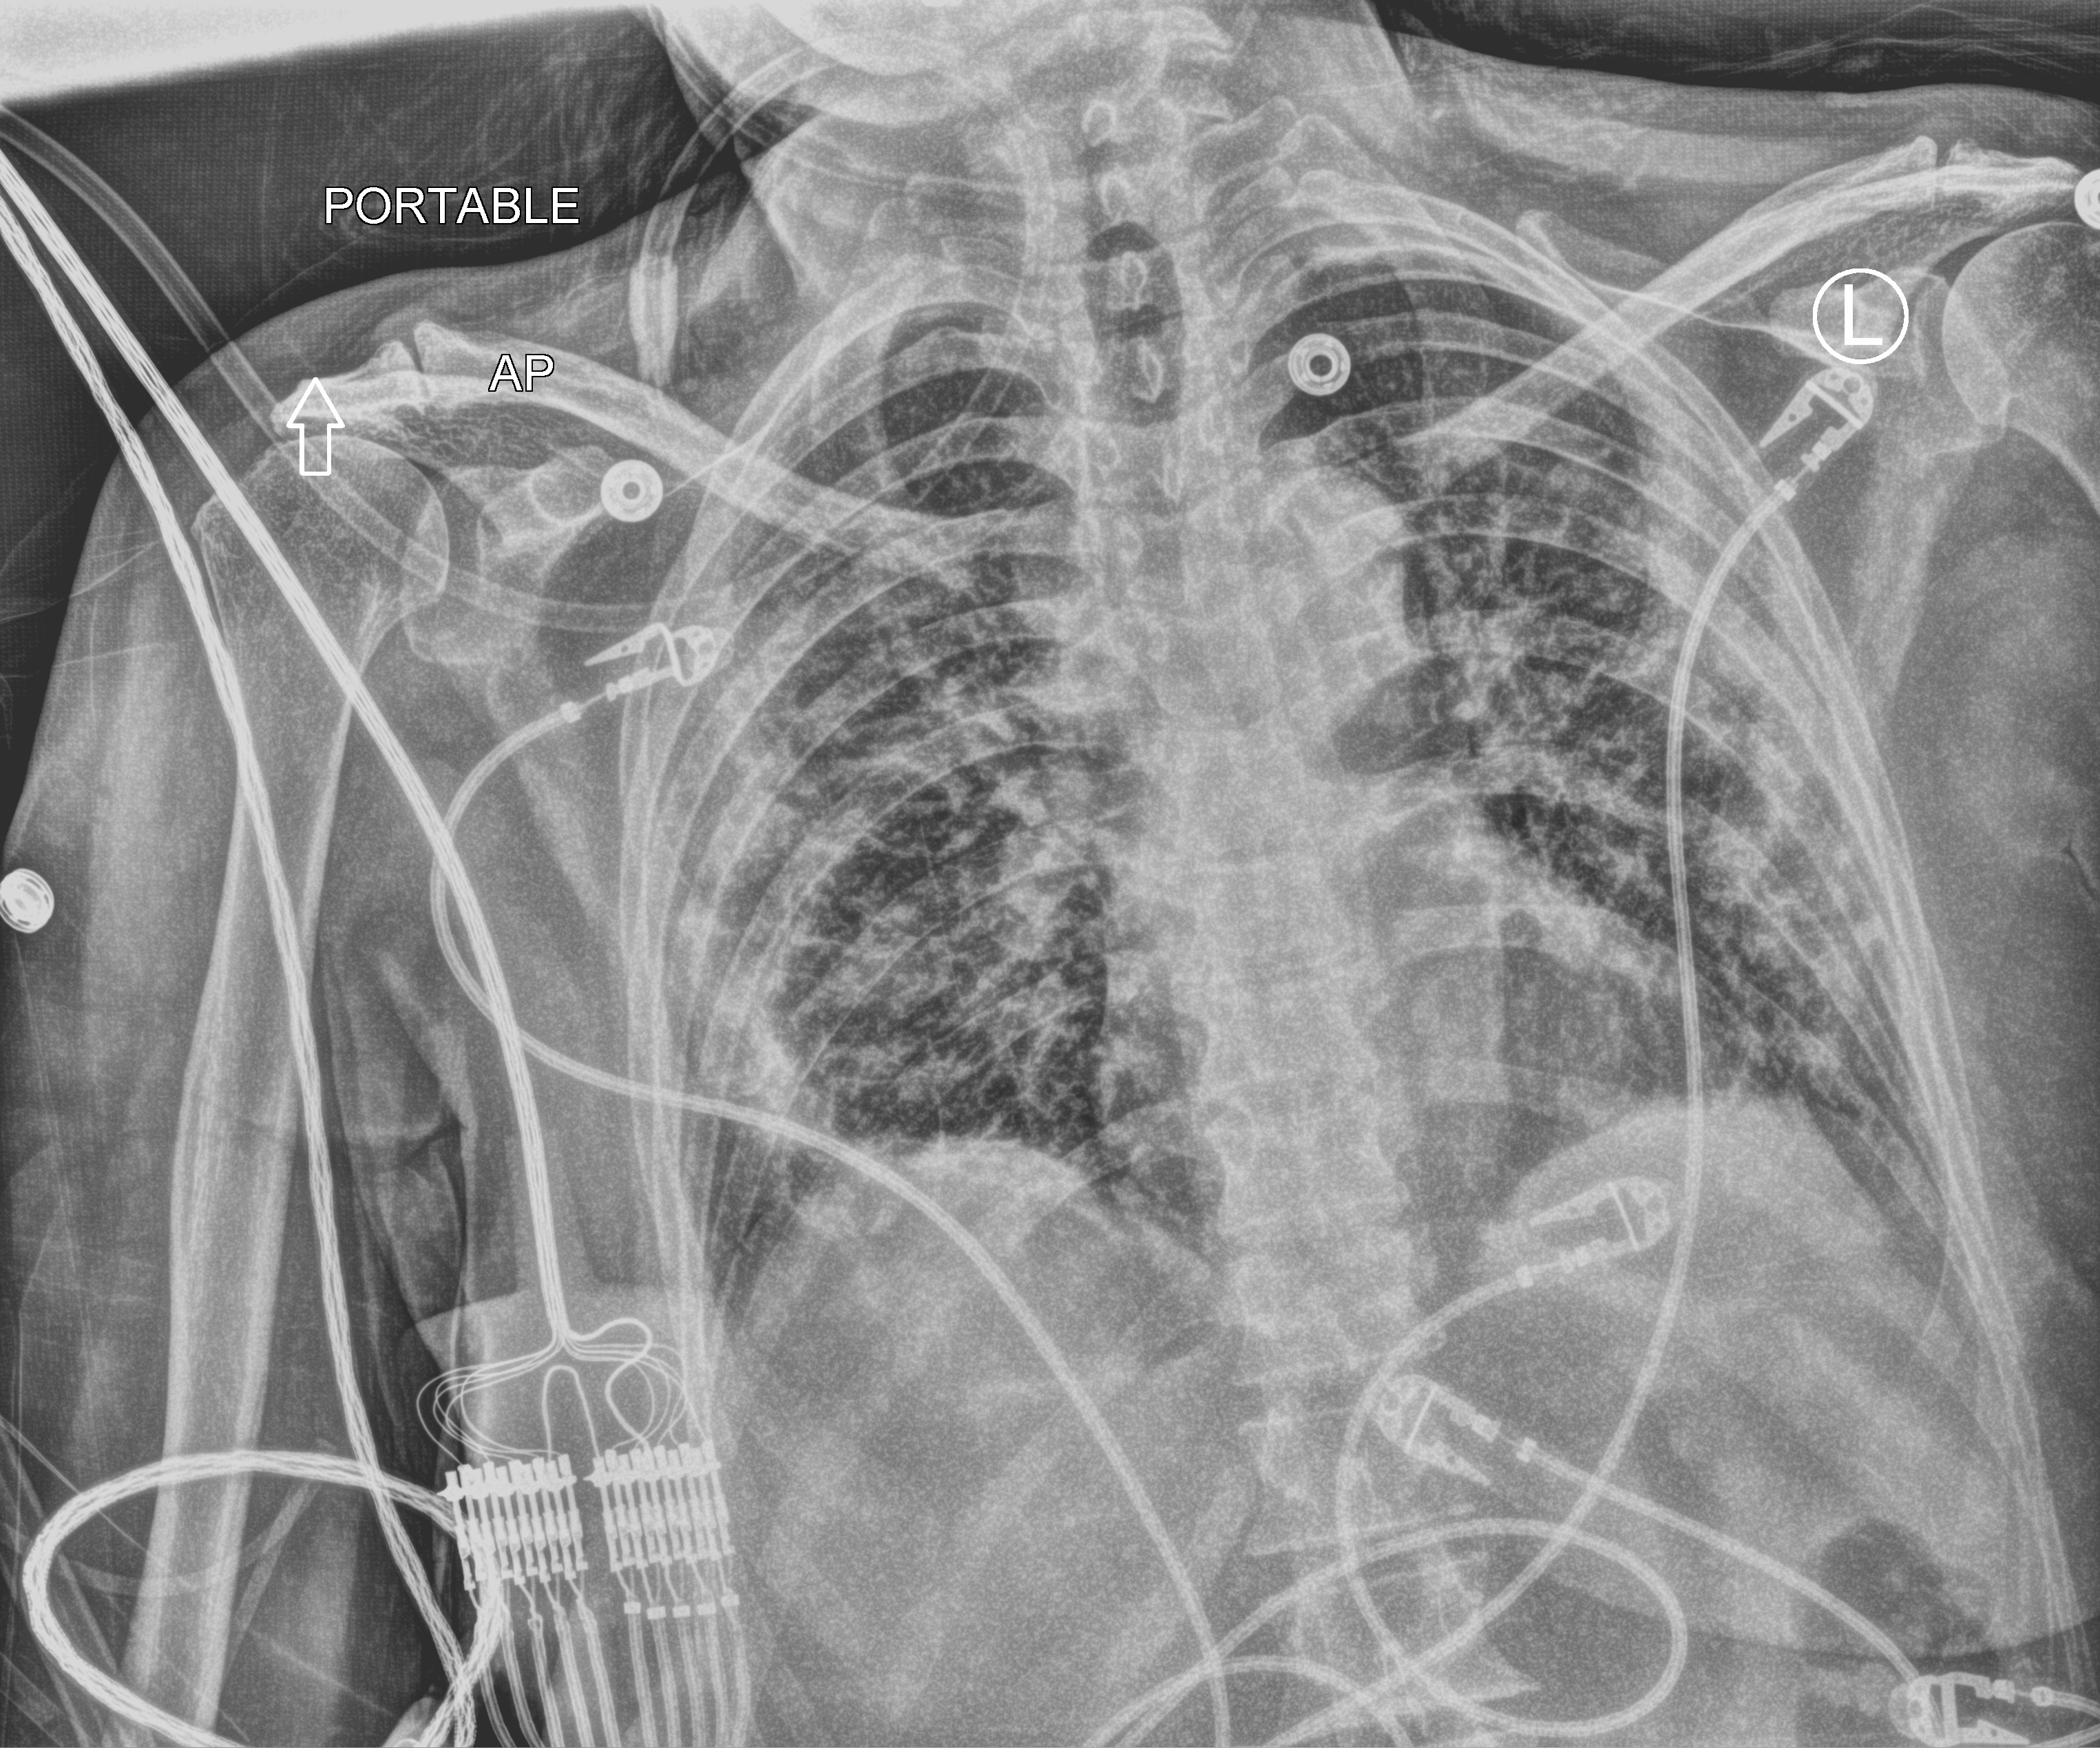
Chest X-ray (portable), anteroposterior (AP) projection. Patient hospitalised with COVID-19; female, aged 60–74 years.
From the hospital-stay record, not from the radiograph (when in the stay this image was taken is not recorded): length of hospital stay: 18 days; mechanically ventilated during this hospital stay: yes.